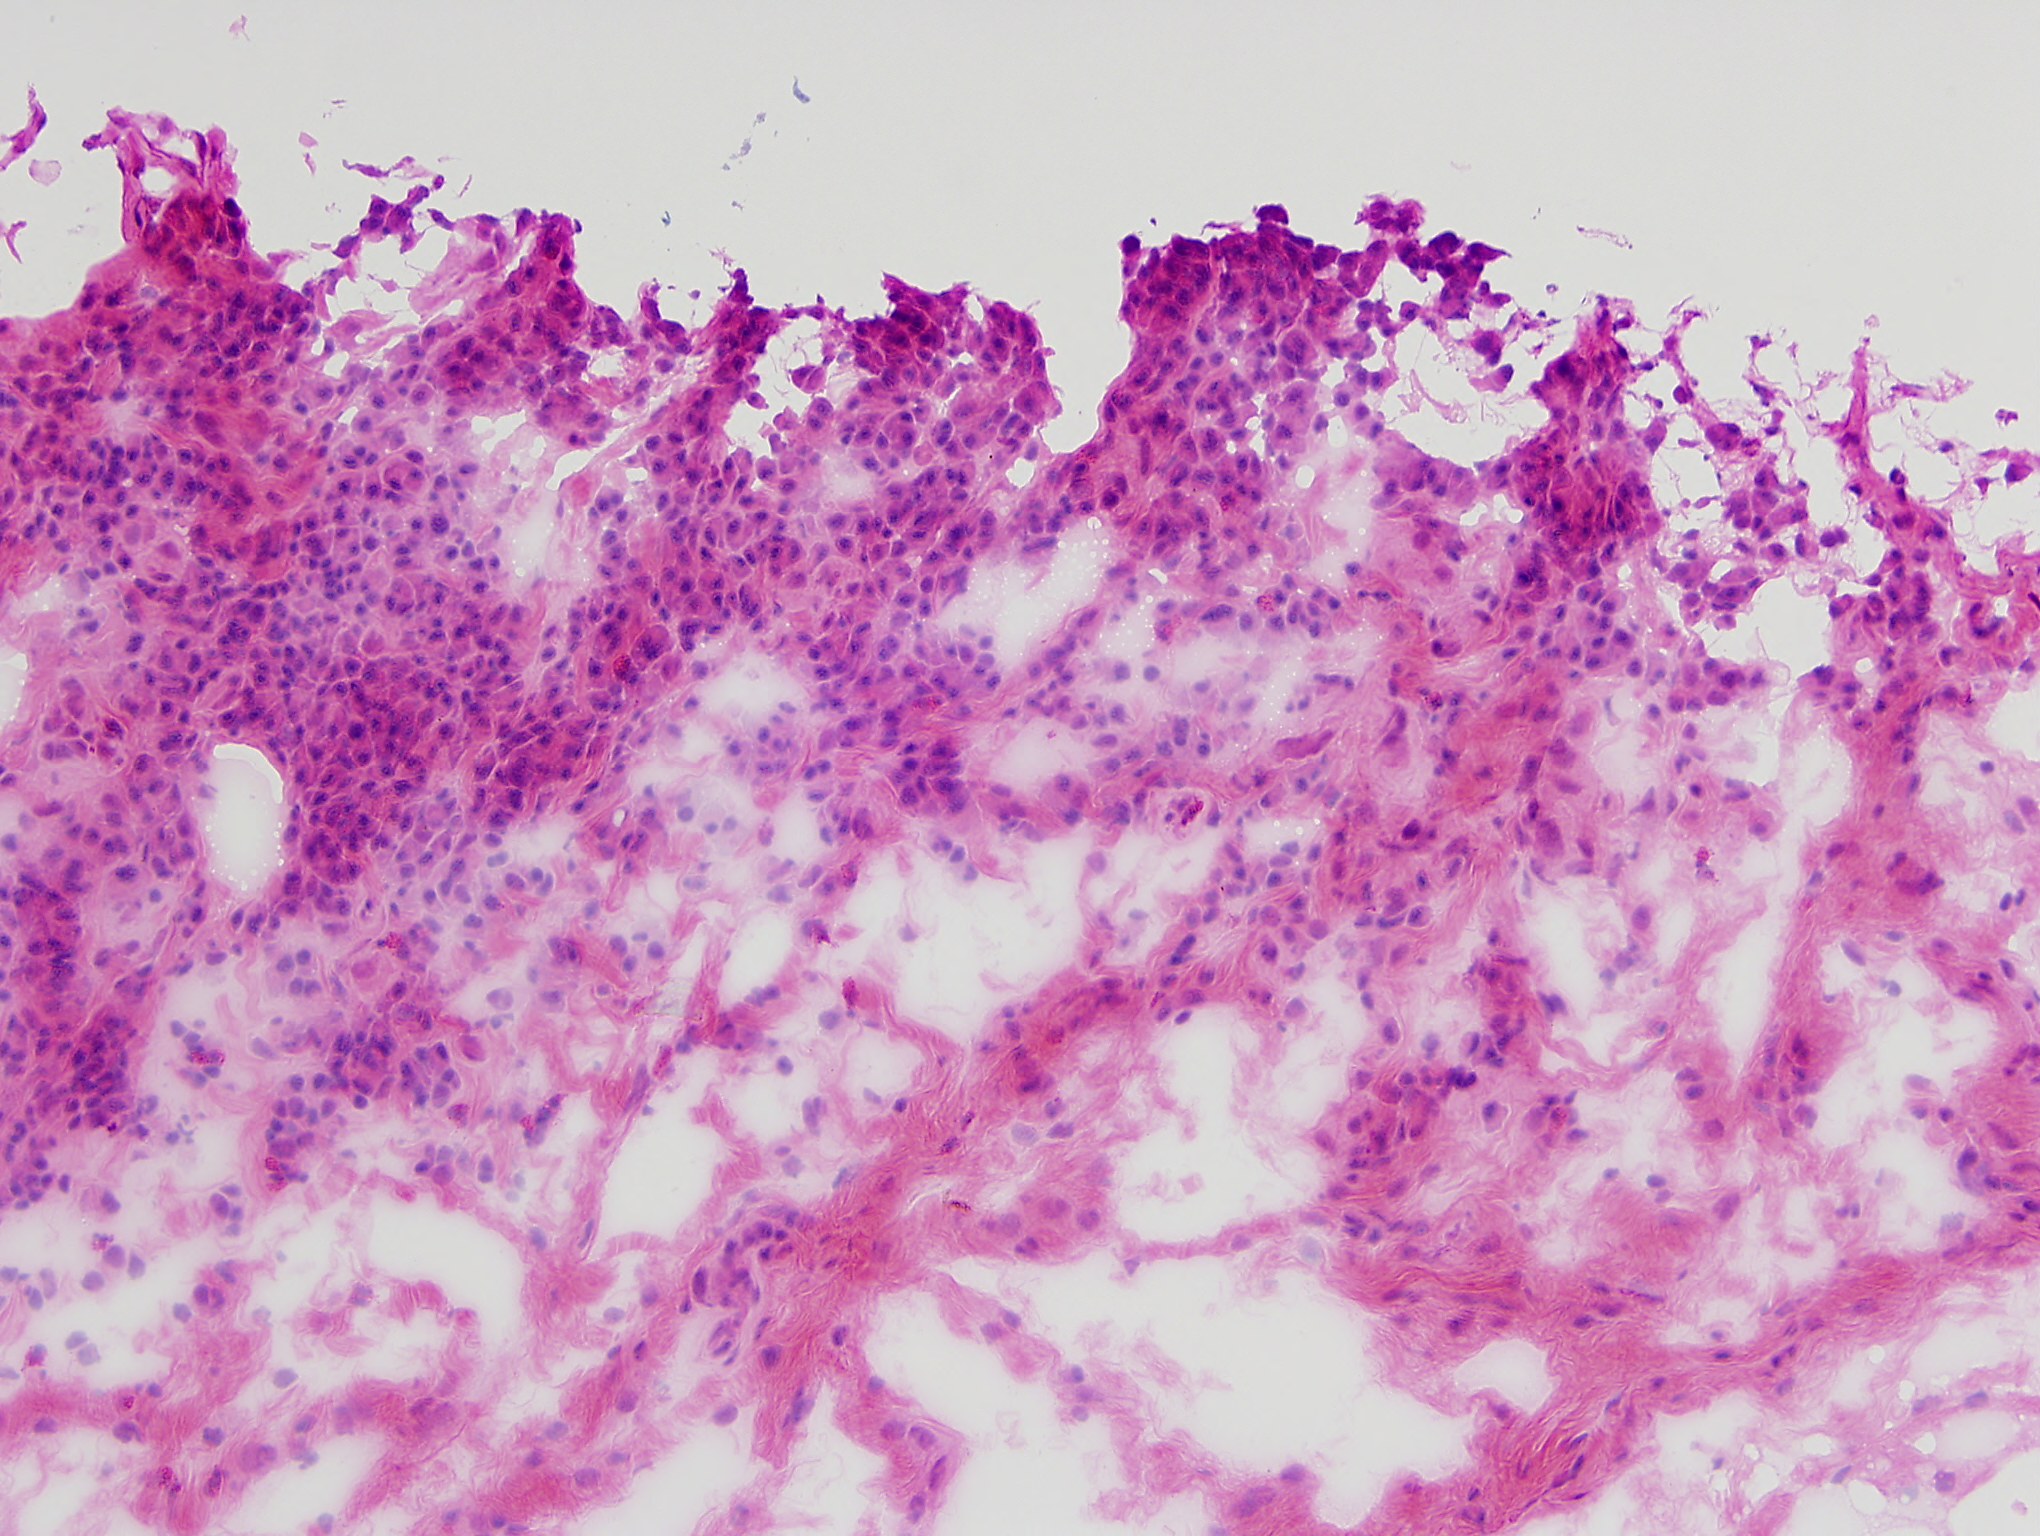
H&E image of one small field of the section — covering about 1.0 x 0.8 mm, frozen section, sample: solid tissue normal (non-tumour tissue), head and neck. Male patient; age at initial diagnosis 49 years.
• this section: solid tissue normal sample (biorepository sample class)
• patient diagnosis: Squamous cell carcinoma, NOS (base of tongue, NOS)